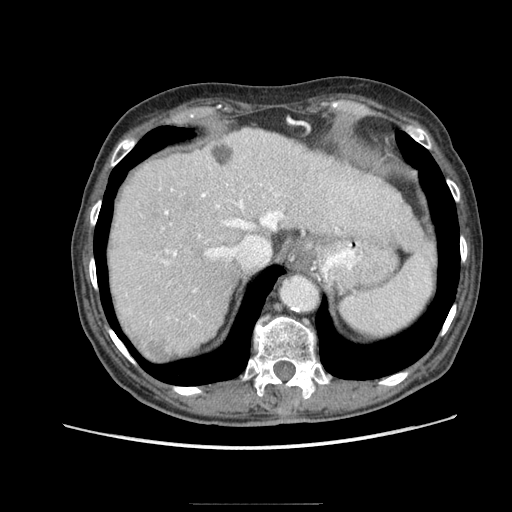
Contrast-enhanced abdominal CT (liver protocol), one axial slice; slice 66 of 83 in the series (ordered by position); reconstruction kernel STANDARD; 140 kVp; soft-tissue window (W 400 / L 40 HU); 512 × 512 image matrix. From the clinical record (not read from this slice): diagnosis: hepatocellular carcinoma (patient treated with transarterial chemoembolisation; whether this scan precedes or follows treatment is not stated here); TNM stage (as recorded): Stage-I; Child-Pugh class: A; tumour differentiation: moderately differentiated.
Outlined on this slice (semi-automatic segmentation, software-assisted and operator-edited):
- abdominal aorta: bounding box [x1, y1, x2, y2] px = [280, 276, 318, 312]
- liver parenchyma outside the tumour (the mass and vessels are separate outlines, so this box may not span the whole liver): [108, 128, 422, 356]
- mass: [146, 340, 171, 363]
- liver vessels: [164, 187, 338, 317]